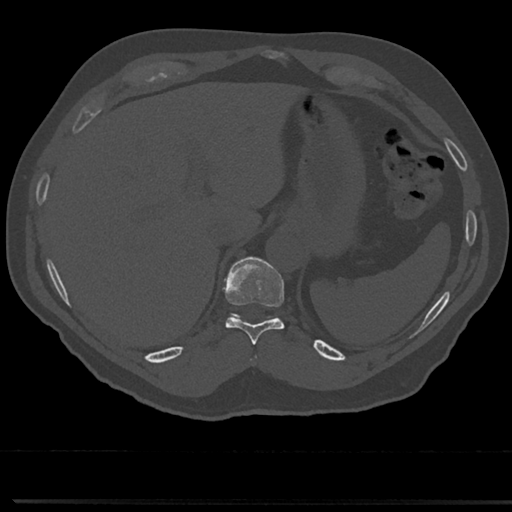
CT including the spine, one axial slice; slice 248 of 817 in the series (ordered by position); reconstruction kernel Br40s/3; bone window (W 1800 / L 400 HU); 512 × 512 image matrix, field of view 355 × 355 mm. Male patient, age 61 years. From the clinical record (not read from this slice): primary cancer: prostate.
Structures marked on this image (semi-automatically segmented with operator editing):
- T10 vertebra: bounding box (x1, y1, x2, y2) in pixels: (223, 257, 287, 343)
- T9 vertebra: (250, 353, 259, 366)